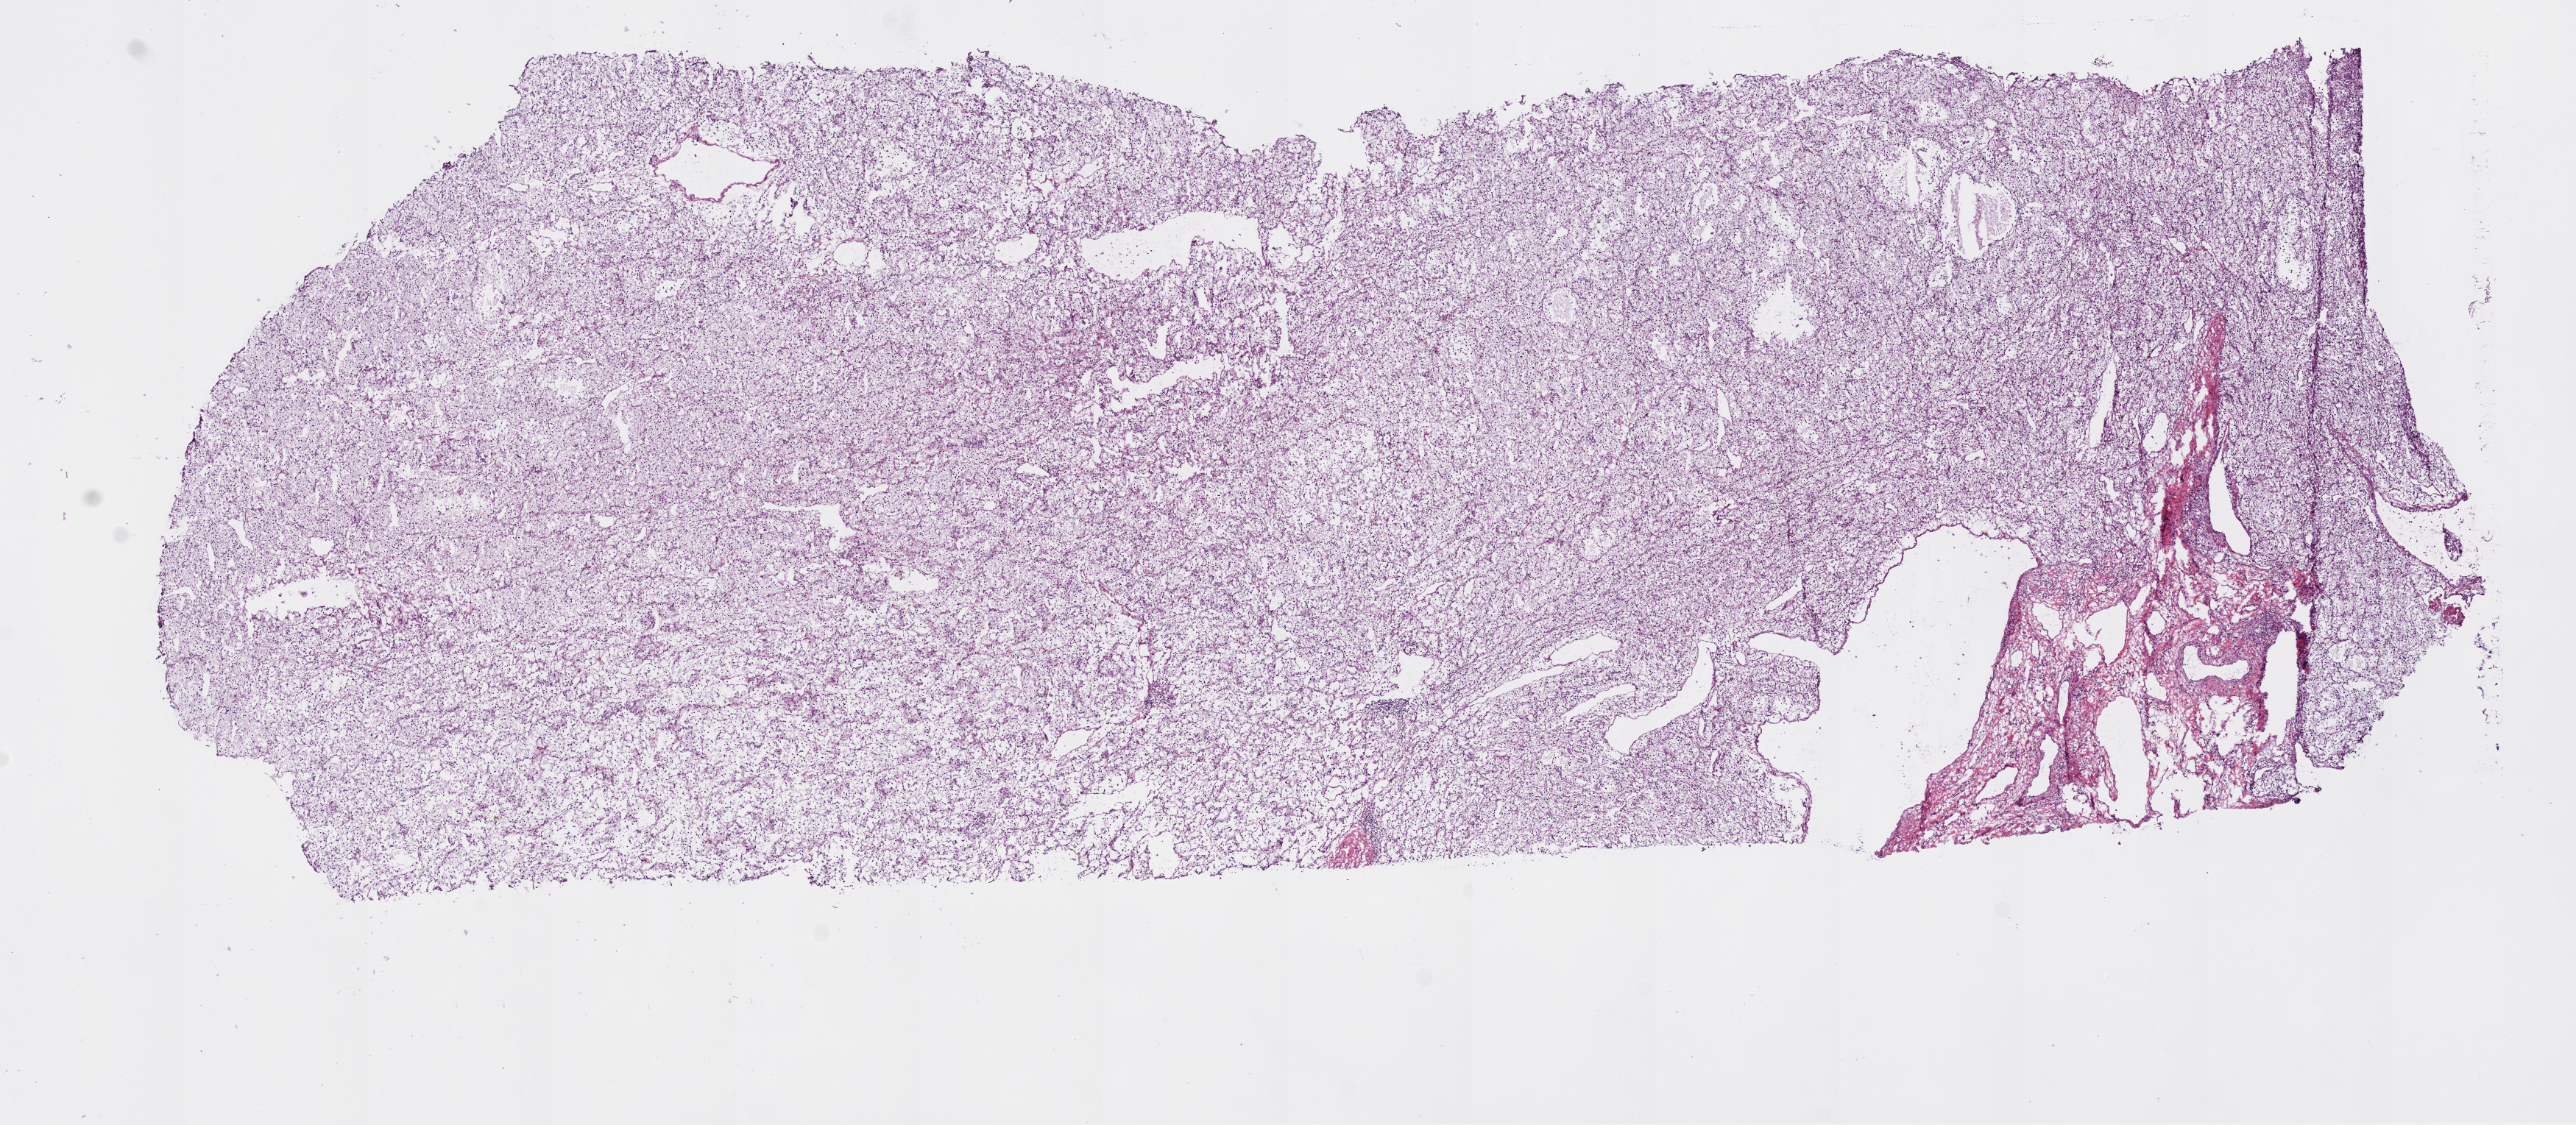
Whole-slide histology image, H&E, a low-resolution overview of the entire scanned area, about 14.0 x 6.1 mm (acquisition: 20x scan). Frozen section from the bottom of the tissue portion. Sample: primary tumour, kidney. Female patient; age at initial diagnosis 62 years.
Diagnosis: Clear cell adenocarcinoma, NOS.